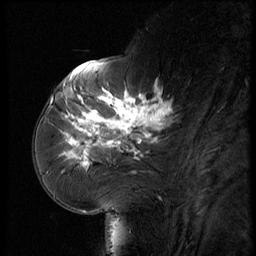
Breast MRI (dynamic contrast-enhanced), one sagittal slice; position 23 of 56 along the scan axis; dynamic contrast-enhanced series, image 2 of 3 at this slice position (ordered by acquisition); 1.5 T; TE 4.2 ms, TR 9 ms; 256 × 256 image matrix. Female patient, age 61 years. From the clinical record (not read from this slice): setting: breast cancer imaged before/during neoadjuvant chemotherapy; receptor status: HR-positive, HER2-negative.
Outlined on this slice (semi-automatically segmented with operator editing):
- analysis volume of interest (the breast-tissue region the enhancement analysis was run in; not a lesion): bounding box [x1, y1, x2, y2] px = [65, 74, 185, 175]
- tumour enhancement mask (voxels above the 140 % enhancement threshold inside the analysis volume of interest): [65, 85, 173, 168]